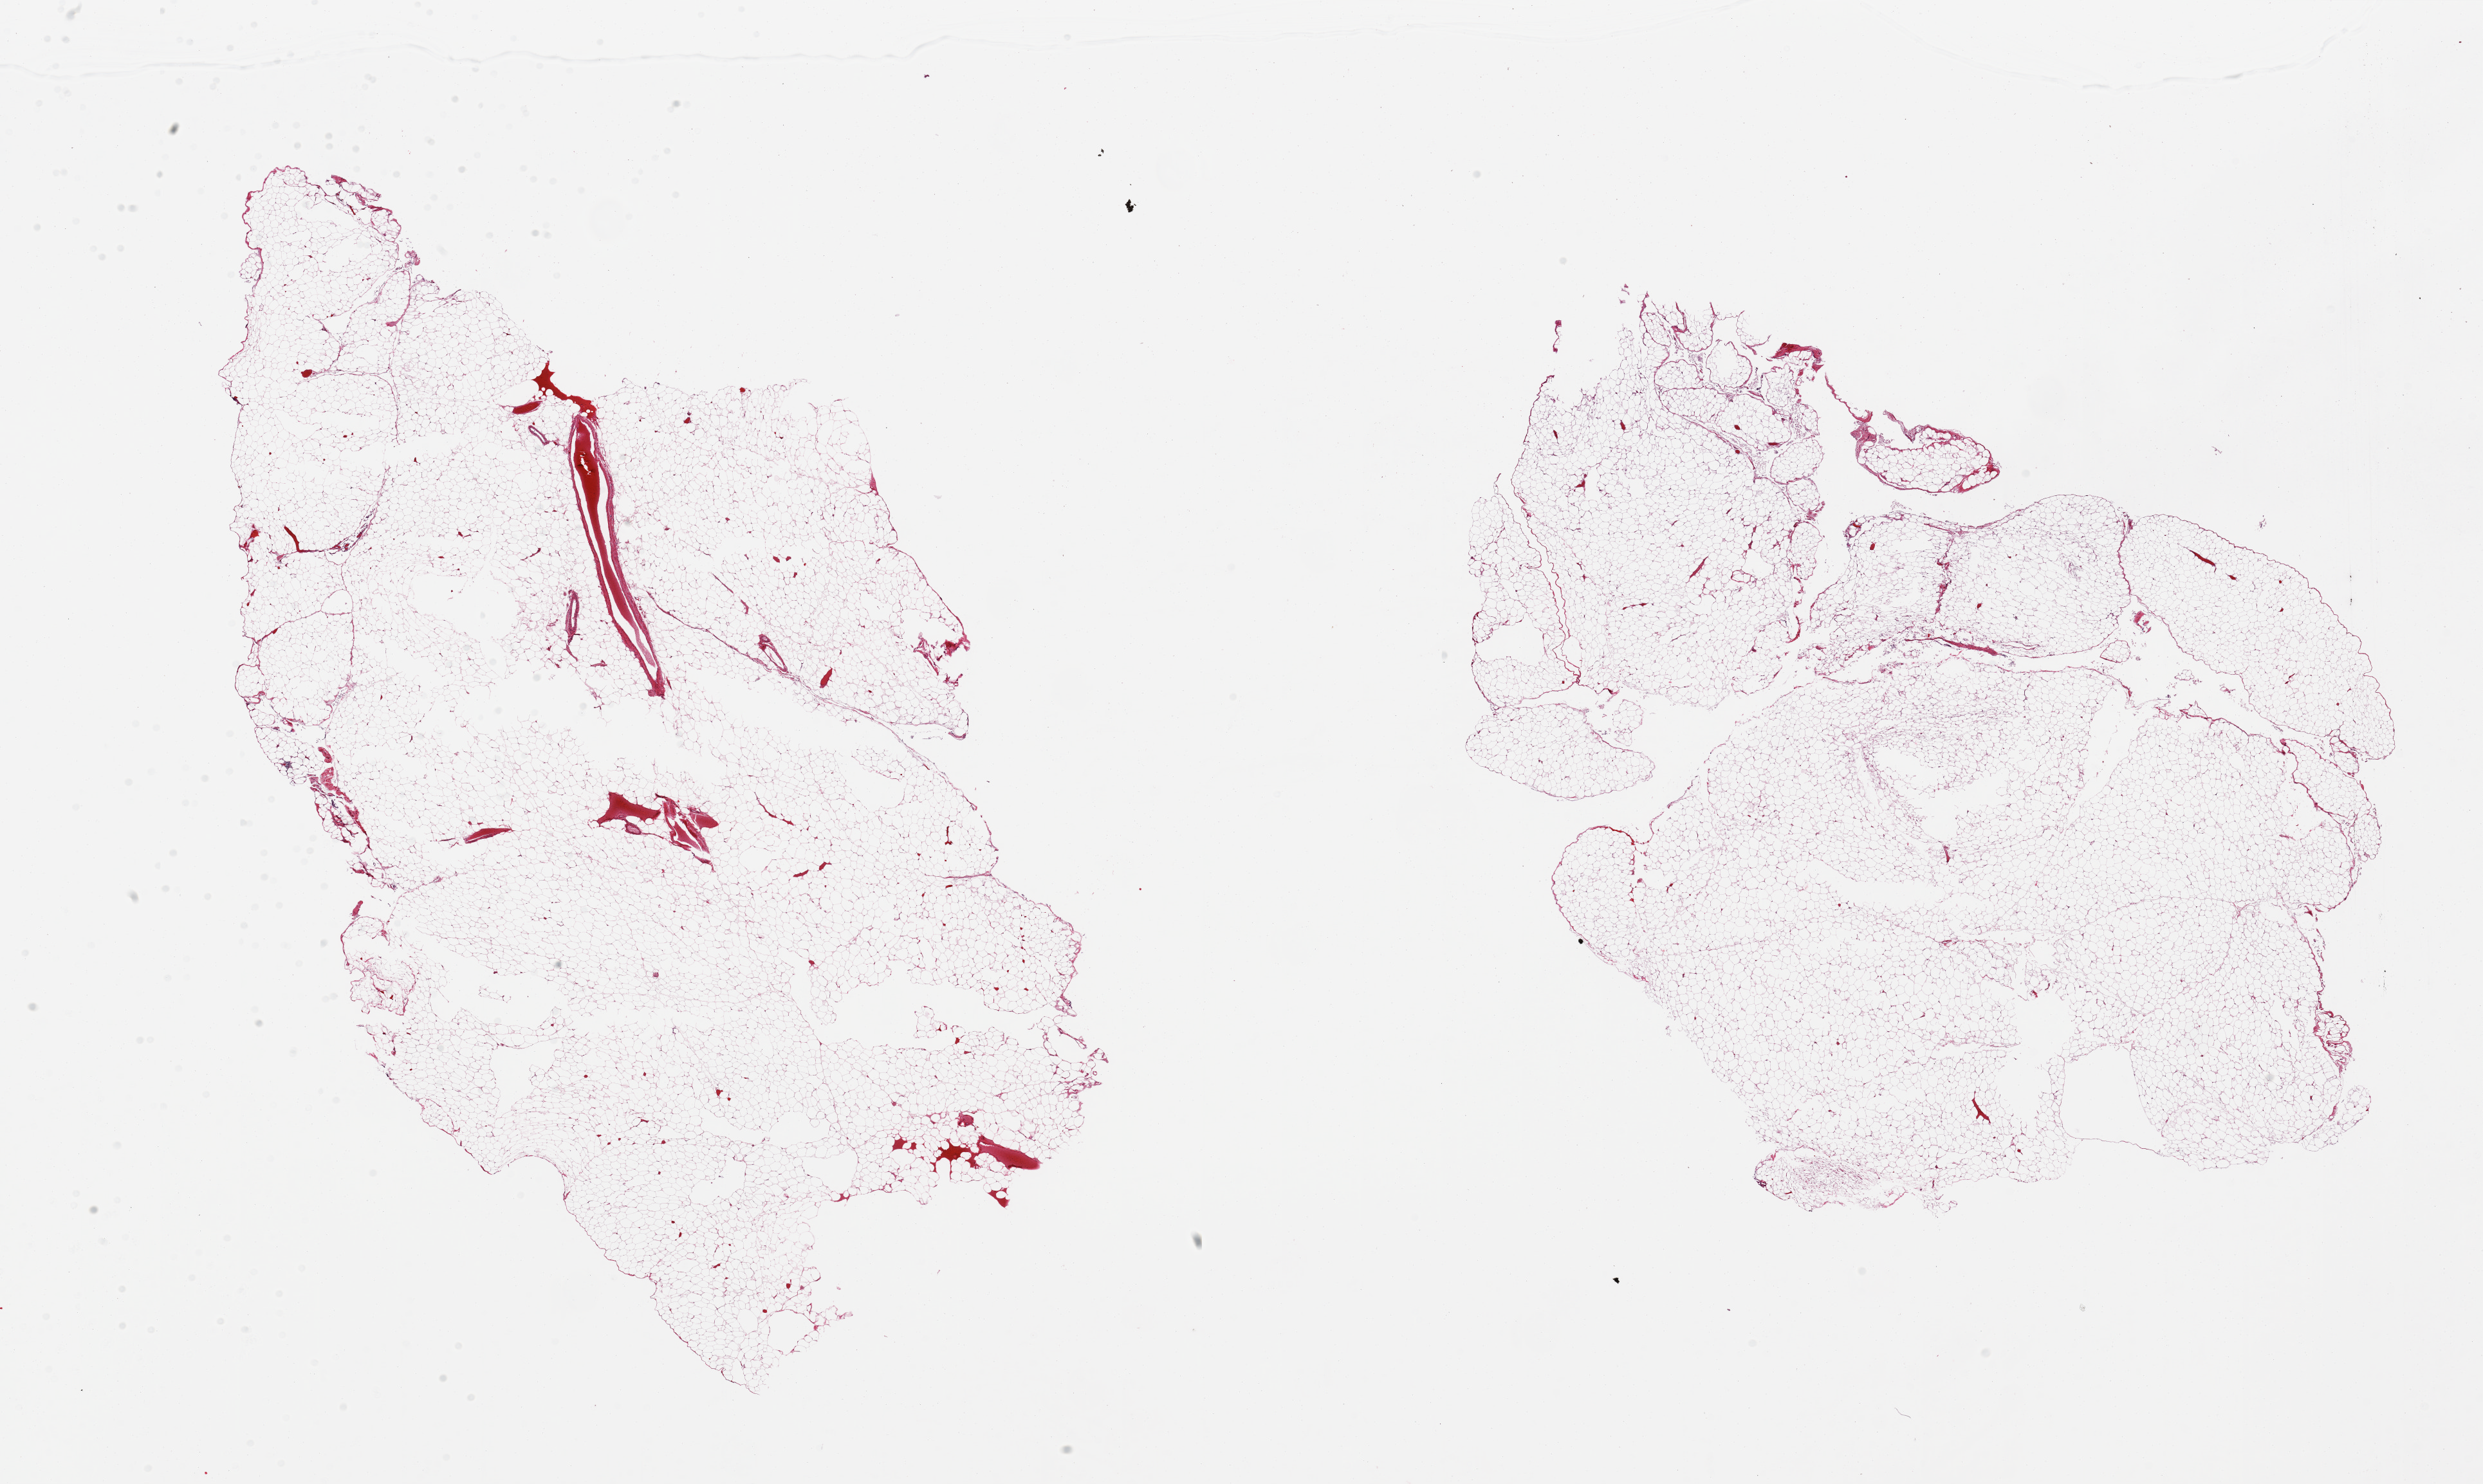
Digitized H&E-stained section, low-resolution overview of the scanned area, about 30.5 x 18.2 mm, PAXgene-fixed, paraffin-embedded tissue, target tissue: omentum, tissue donor sample. Male donor.
Pathologist's review note for this sample: 2 pieces.